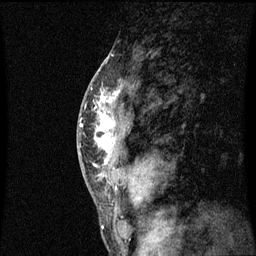
Breast MRI (dynamic contrast-enhanced), one sagittal slice. Dynamic contrast-enhanced series, image 2 of 3 at this slice position (ordered by acquisition). 1.5 T. TE 4.2 ms, TR 8.9 ms. 2 mm slice thickness. 256 × 256 image matrix, field of view 200 × 200 mm. Female patient, age 50 years. Case-level facts recorded for this patient, not image findings: setting: breast cancer imaged before/during neoadjuvant chemotherapy; receptor status: triple-negative.
Structures marked on this image (semi-automatic segmentation, software-assisted and operator-edited):
- analysis volume of interest (the breast-tissue region the enhancement analysis was run in; not a lesion): bounding box (x1, y1, x2, y2) in pixels: (84, 80, 129, 171)
- tumour enhancement mask (voxels above the 70 % enhancement threshold inside the analysis volume of interest): (94, 92, 119, 167)